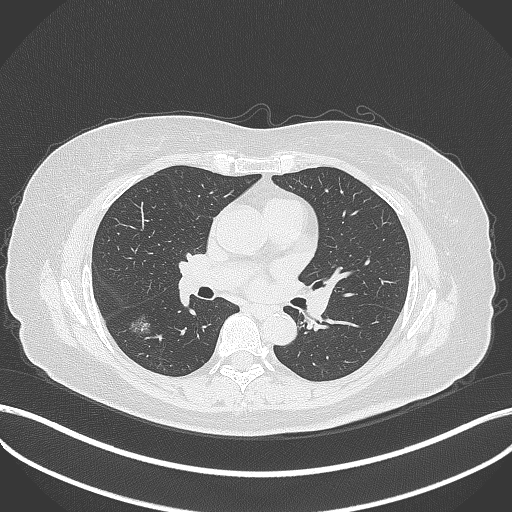
Chest CT, one axial slice. Slice 171 of 322 in the series (ordered by position). 120 kVp. Lung window (W 1500 / L -600 HU). 1 mm slice thickness. 512 × 512 image matrix. Female patient, age 64 years. From the clinical record (not read from this slice): clinical TNM (as recorded): T1c N0 M0; histopathological grade: G1.
Outlined on this slice (bounding box drawn by a radiologist):
- lung tumour (recorded histology: adenocarcinoma): box from (x=125, y=308) to (x=154, y=340) px